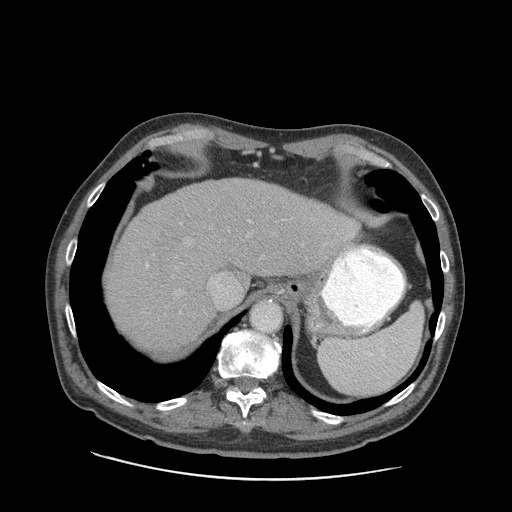
Contrast-enhanced abdominal CT (liver protocol), one axial slice; slice 70 of 89 in the series (ordered by position); 140 kVp; soft-tissue window (W 400 / L 40 HU); 2.5 mm slice thickness; 512 × 512 image matrix, field of view 420 × 420 mm. From the clinical record (not read from this slice): diagnosis: hepatocellular carcinoma (patient treated with transarterial chemoembolisation; whether this scan precedes or follows treatment is not stated here); TNM stage (as recorded): Stage-I; Child-Pugh class: A; tumour differentiation: moderately differentiated; tumour nodularity: uninodular.
Annotated regions visible in this slice (semi-automatic segmentation, software-assisted and operator-edited):
- liver parenchyma outside the tumour (the mass and vessels are separate outlines, so this box may not span the whole liver): bounding box (x1, y1, x2, y2) in pixels: (106, 178, 358, 352)
- liver vessels: (146, 219, 355, 313)